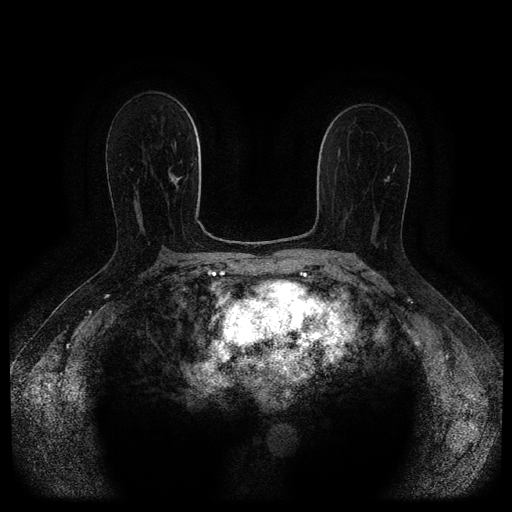
Breast MRI (dynamic contrast-enhanced, multi-phase), one axial slice. Slice 61 of 116 in the series (ordered by position). Dynamic contrast-enhanced series, time point 2 of 5 at this slice position (early post-contrast). 1.5 T. TE 2.7 ms, TR 5.4 ms. 2 mm slice thickness. 512 × 512 image matrix. Patient: female, 71 years.
Structures marked on this image (semi-automatically segmented with operator editing):
- breast lesion (labelled 'tumour' in the annotation; benign lesions carry a separate 'benign' label): box from (x=169, y=173) to (x=182, y=187) px